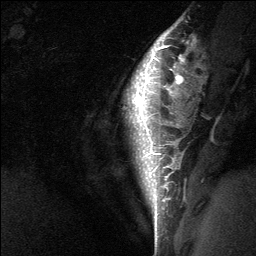
Breast MRI (dynamic contrast-enhanced), one sagittal slice; slice 52 of 64 in the series (ordered by position); dynamic contrast-enhanced study with each time point stored as its own series, time point 2 of 3 at this slice position (early post-contrast, ordered by acquisition time); 1.5 T; TE 4.8 ms, TR 27 ms; 2 mm slice thickness; 256 × 256 image matrix. Patient: female, 26 years. From the clinical record (not read from this slice): setting: breast cancer imaged before/during neoadjuvant chemotherapy; receptor status: HR-positive, HER2-negative.
Structures marked on this image (semi-automatic segmentation, software-assisted and operator-edited):
- analysis volume of interest (the breast-tissue region the enhancement analysis was run in; not a lesion): box from (x=126, y=43) to (x=183, y=138) px
- tumour enhancement mask (voxels above the 90 % enhancement threshold inside the analysis volume of interest): (x=134, y=47)–(x=179, y=102)